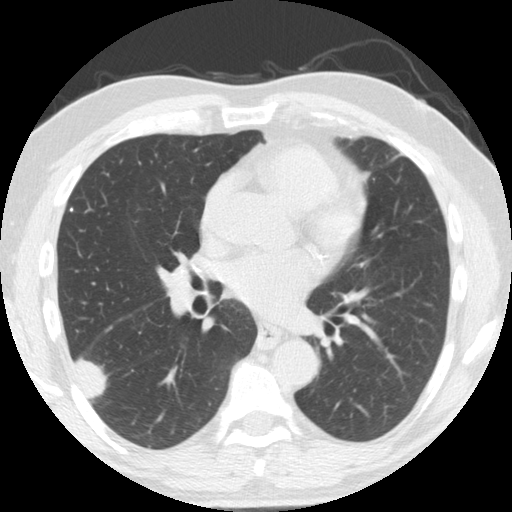
Chest CT (low-dose screening protocol), one axial image. Second screening round (one year after baseline). Lung window (W 1500 / L -600 HU). Slice 90 of 174 in the series. Male, age 61 years at enrolment.
• Lesion marked by an expert reader, bounding box <53,328,120,402> (left, top, right, bottom; pixels).
• The exam's reader record, not a measurement of the box and not confirmed to be the same lesion: non-calcified nodule or mass ≥4 mm, right lower lobe, 33 × 19 mm, smooth margins, soft tissue attenuation, pre-existing on the prior screen: yes; interval growth: yes.
• Participant outcome: lung cancer diagnosed 30 days after this screen — adenosquamous carcinoma, right lower lobe, poorly differentiated (G3), stage IV (AJCC 6th edition), 45 mm at pathology.